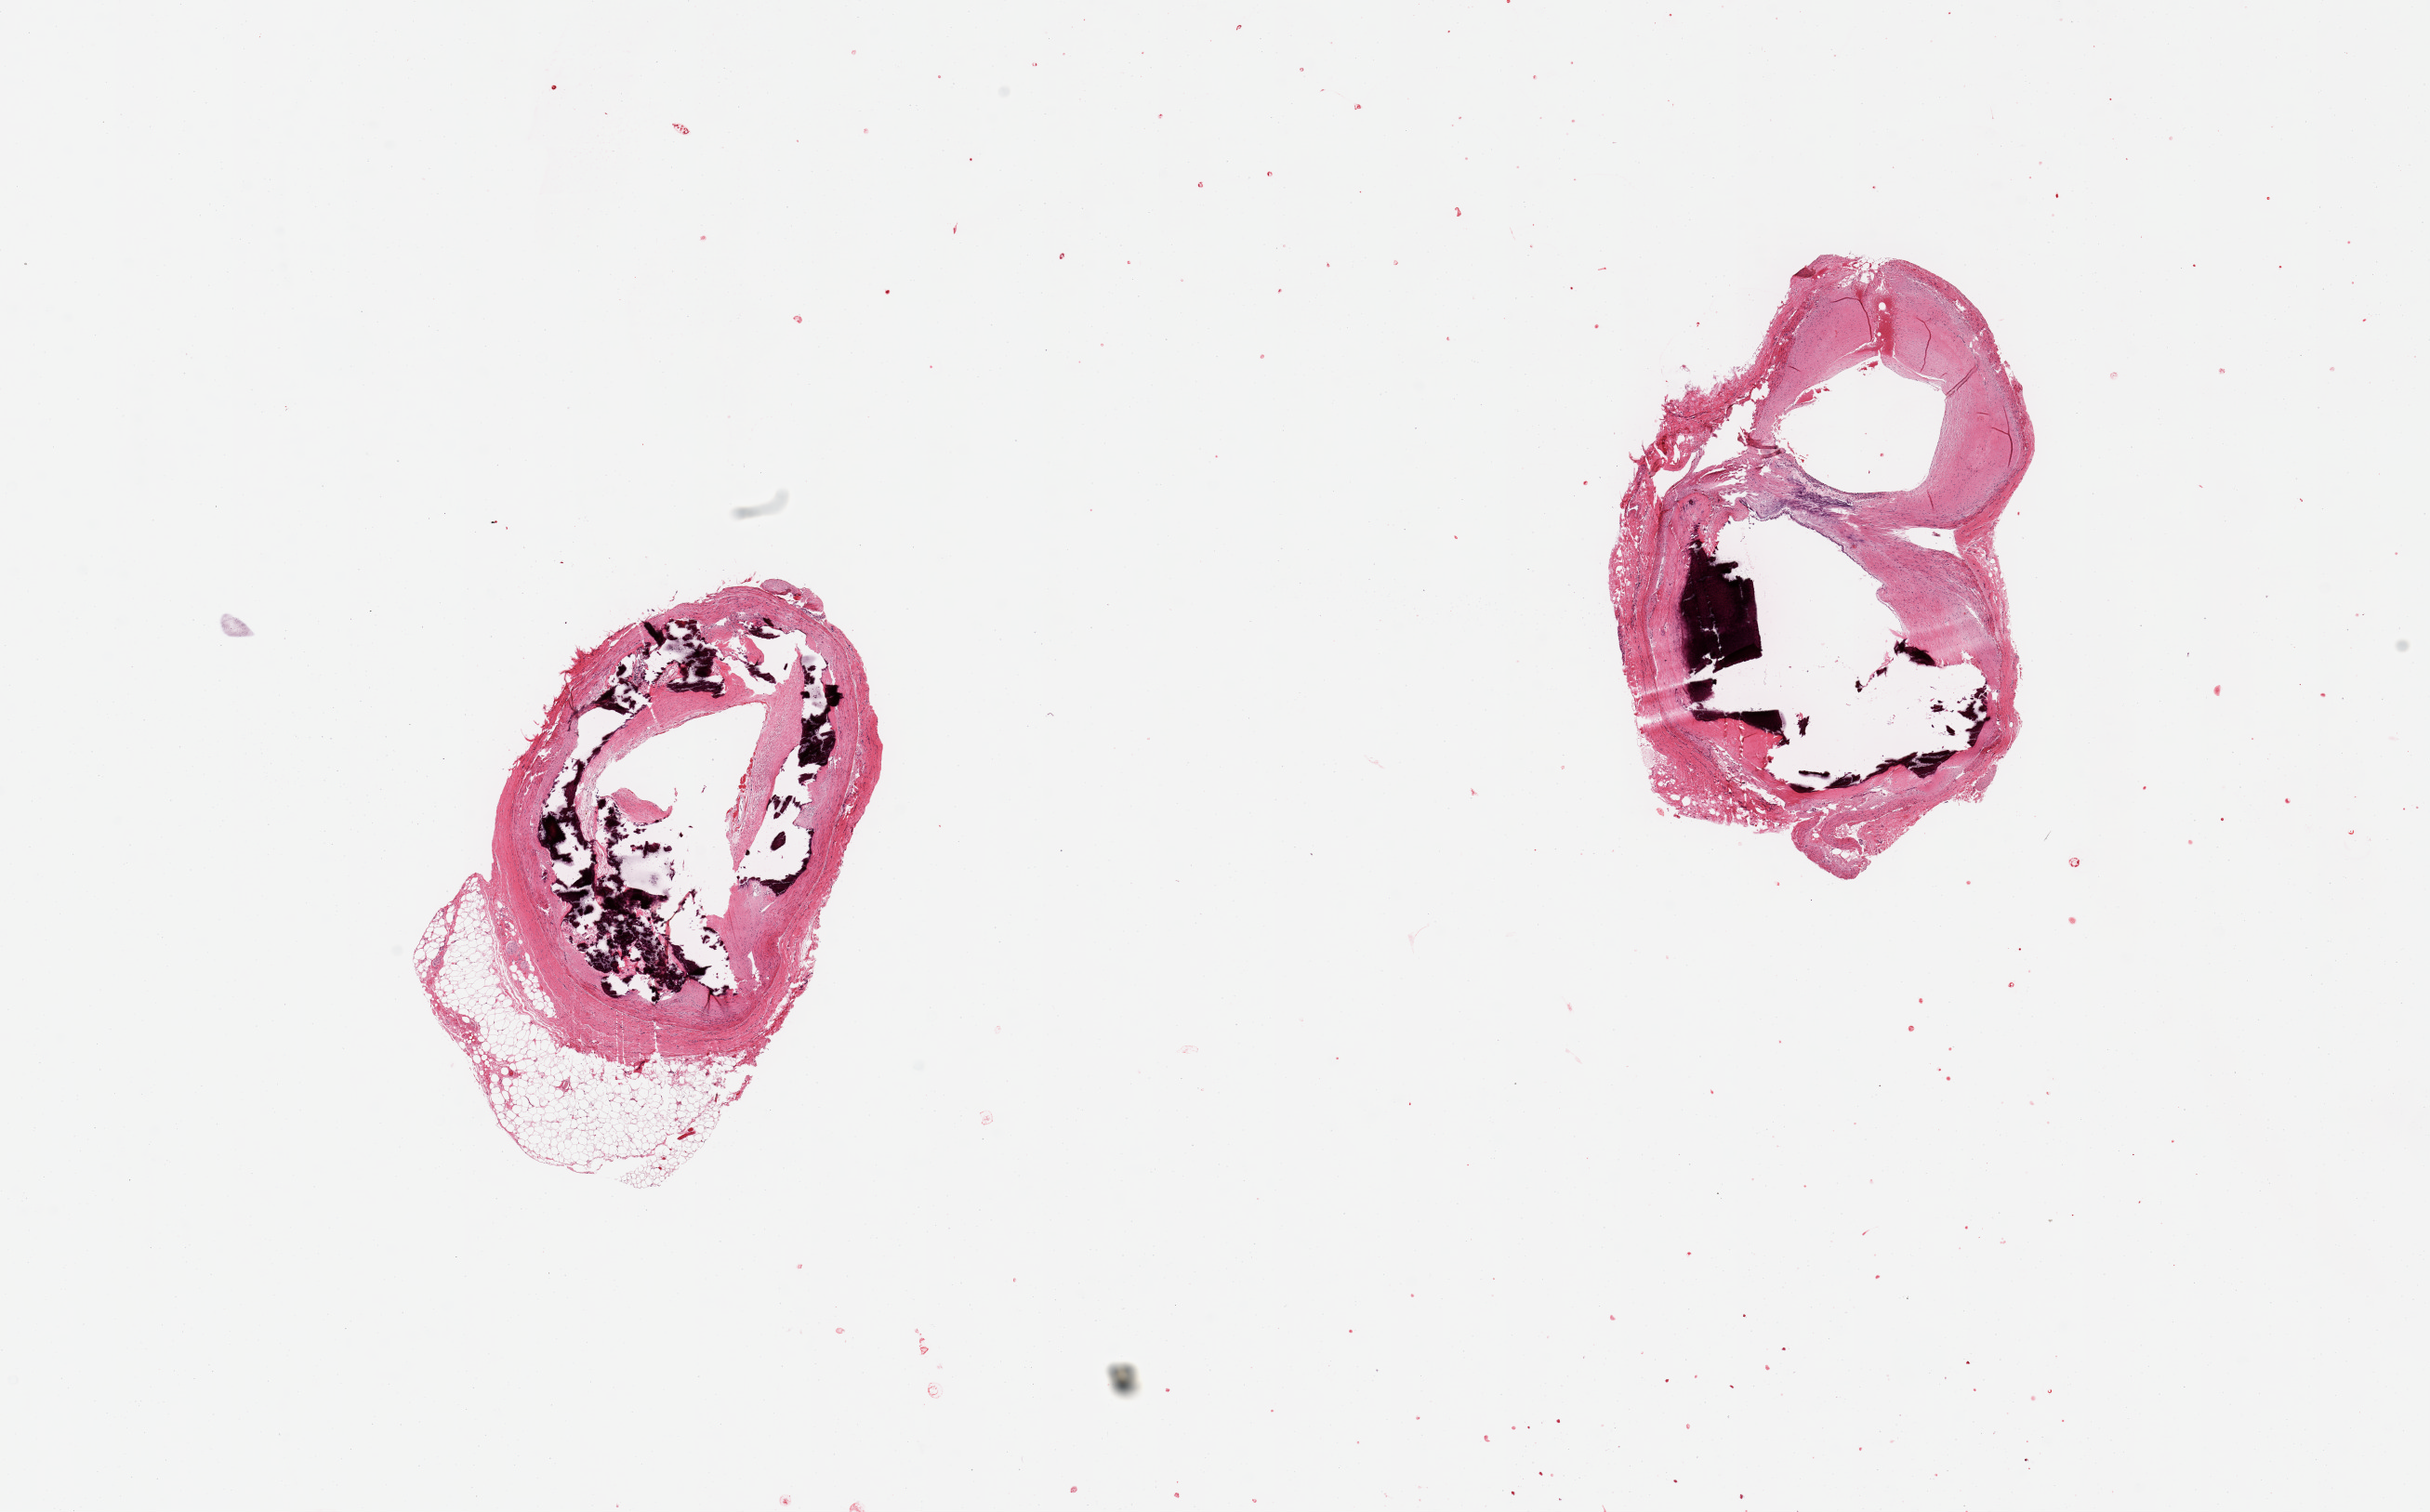
Digitized H&E-stained section — whole scanned area (about 20.7 x 12.9 mm) shown as a low-resolution overview, PAXgene-fixed, paraffin-embedded tissue, sampled site (target tissue): coronary artery, tissue donor sample. Male donor.
* pathologist's review note for this sample: 2 pieces; massive medial calcification and fibrosclerotic plaques with ~75% luminal compromise; focal red blood cell extravasation into the fibrosclerotic plaque; ~1mm attached external fat to one sample